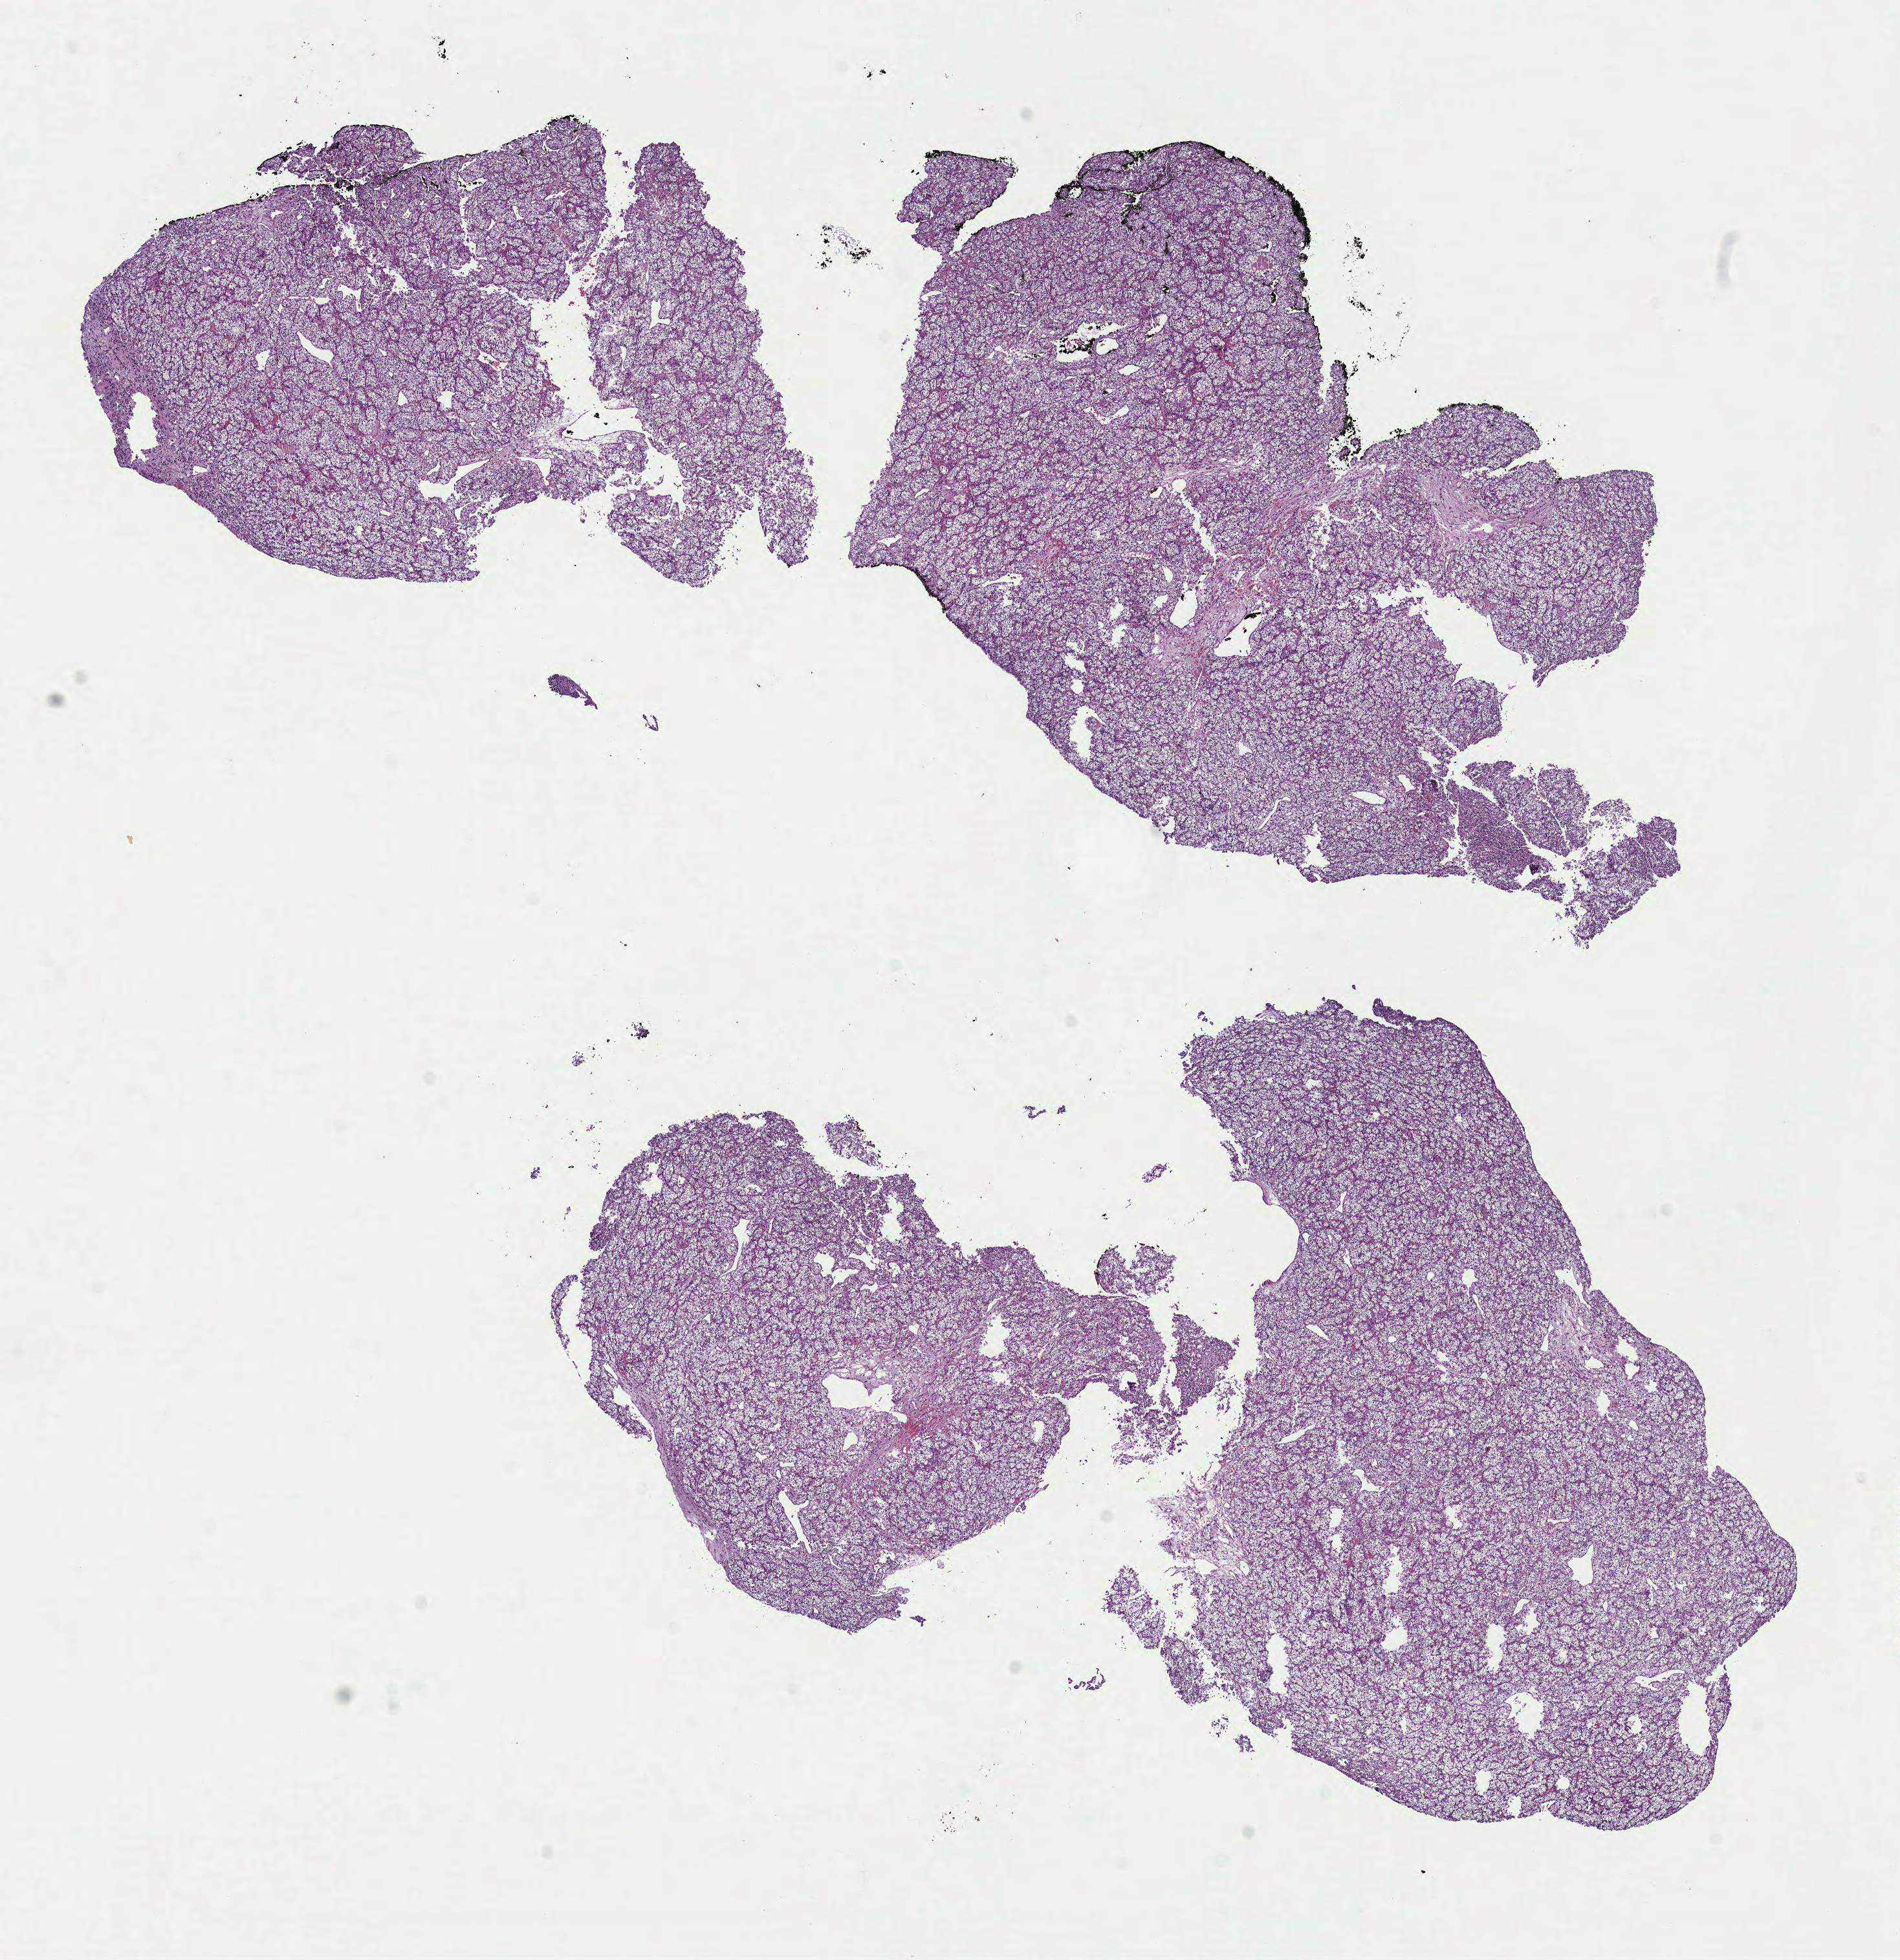
Hematoxylin and eosin (H&E) stained whole-slide image — a low-resolution overview of the entire scanned area, about 11.8 x 12.2 mm (acquisition: 40x scan); formalin-fixed paraffin-embedded (FFPE) diagnostic section; kidney, primary tumour sample. Male, age 78 years at initial diagnosis.
Pathologic diagnosis: Renal cell carcinoma, NOS.